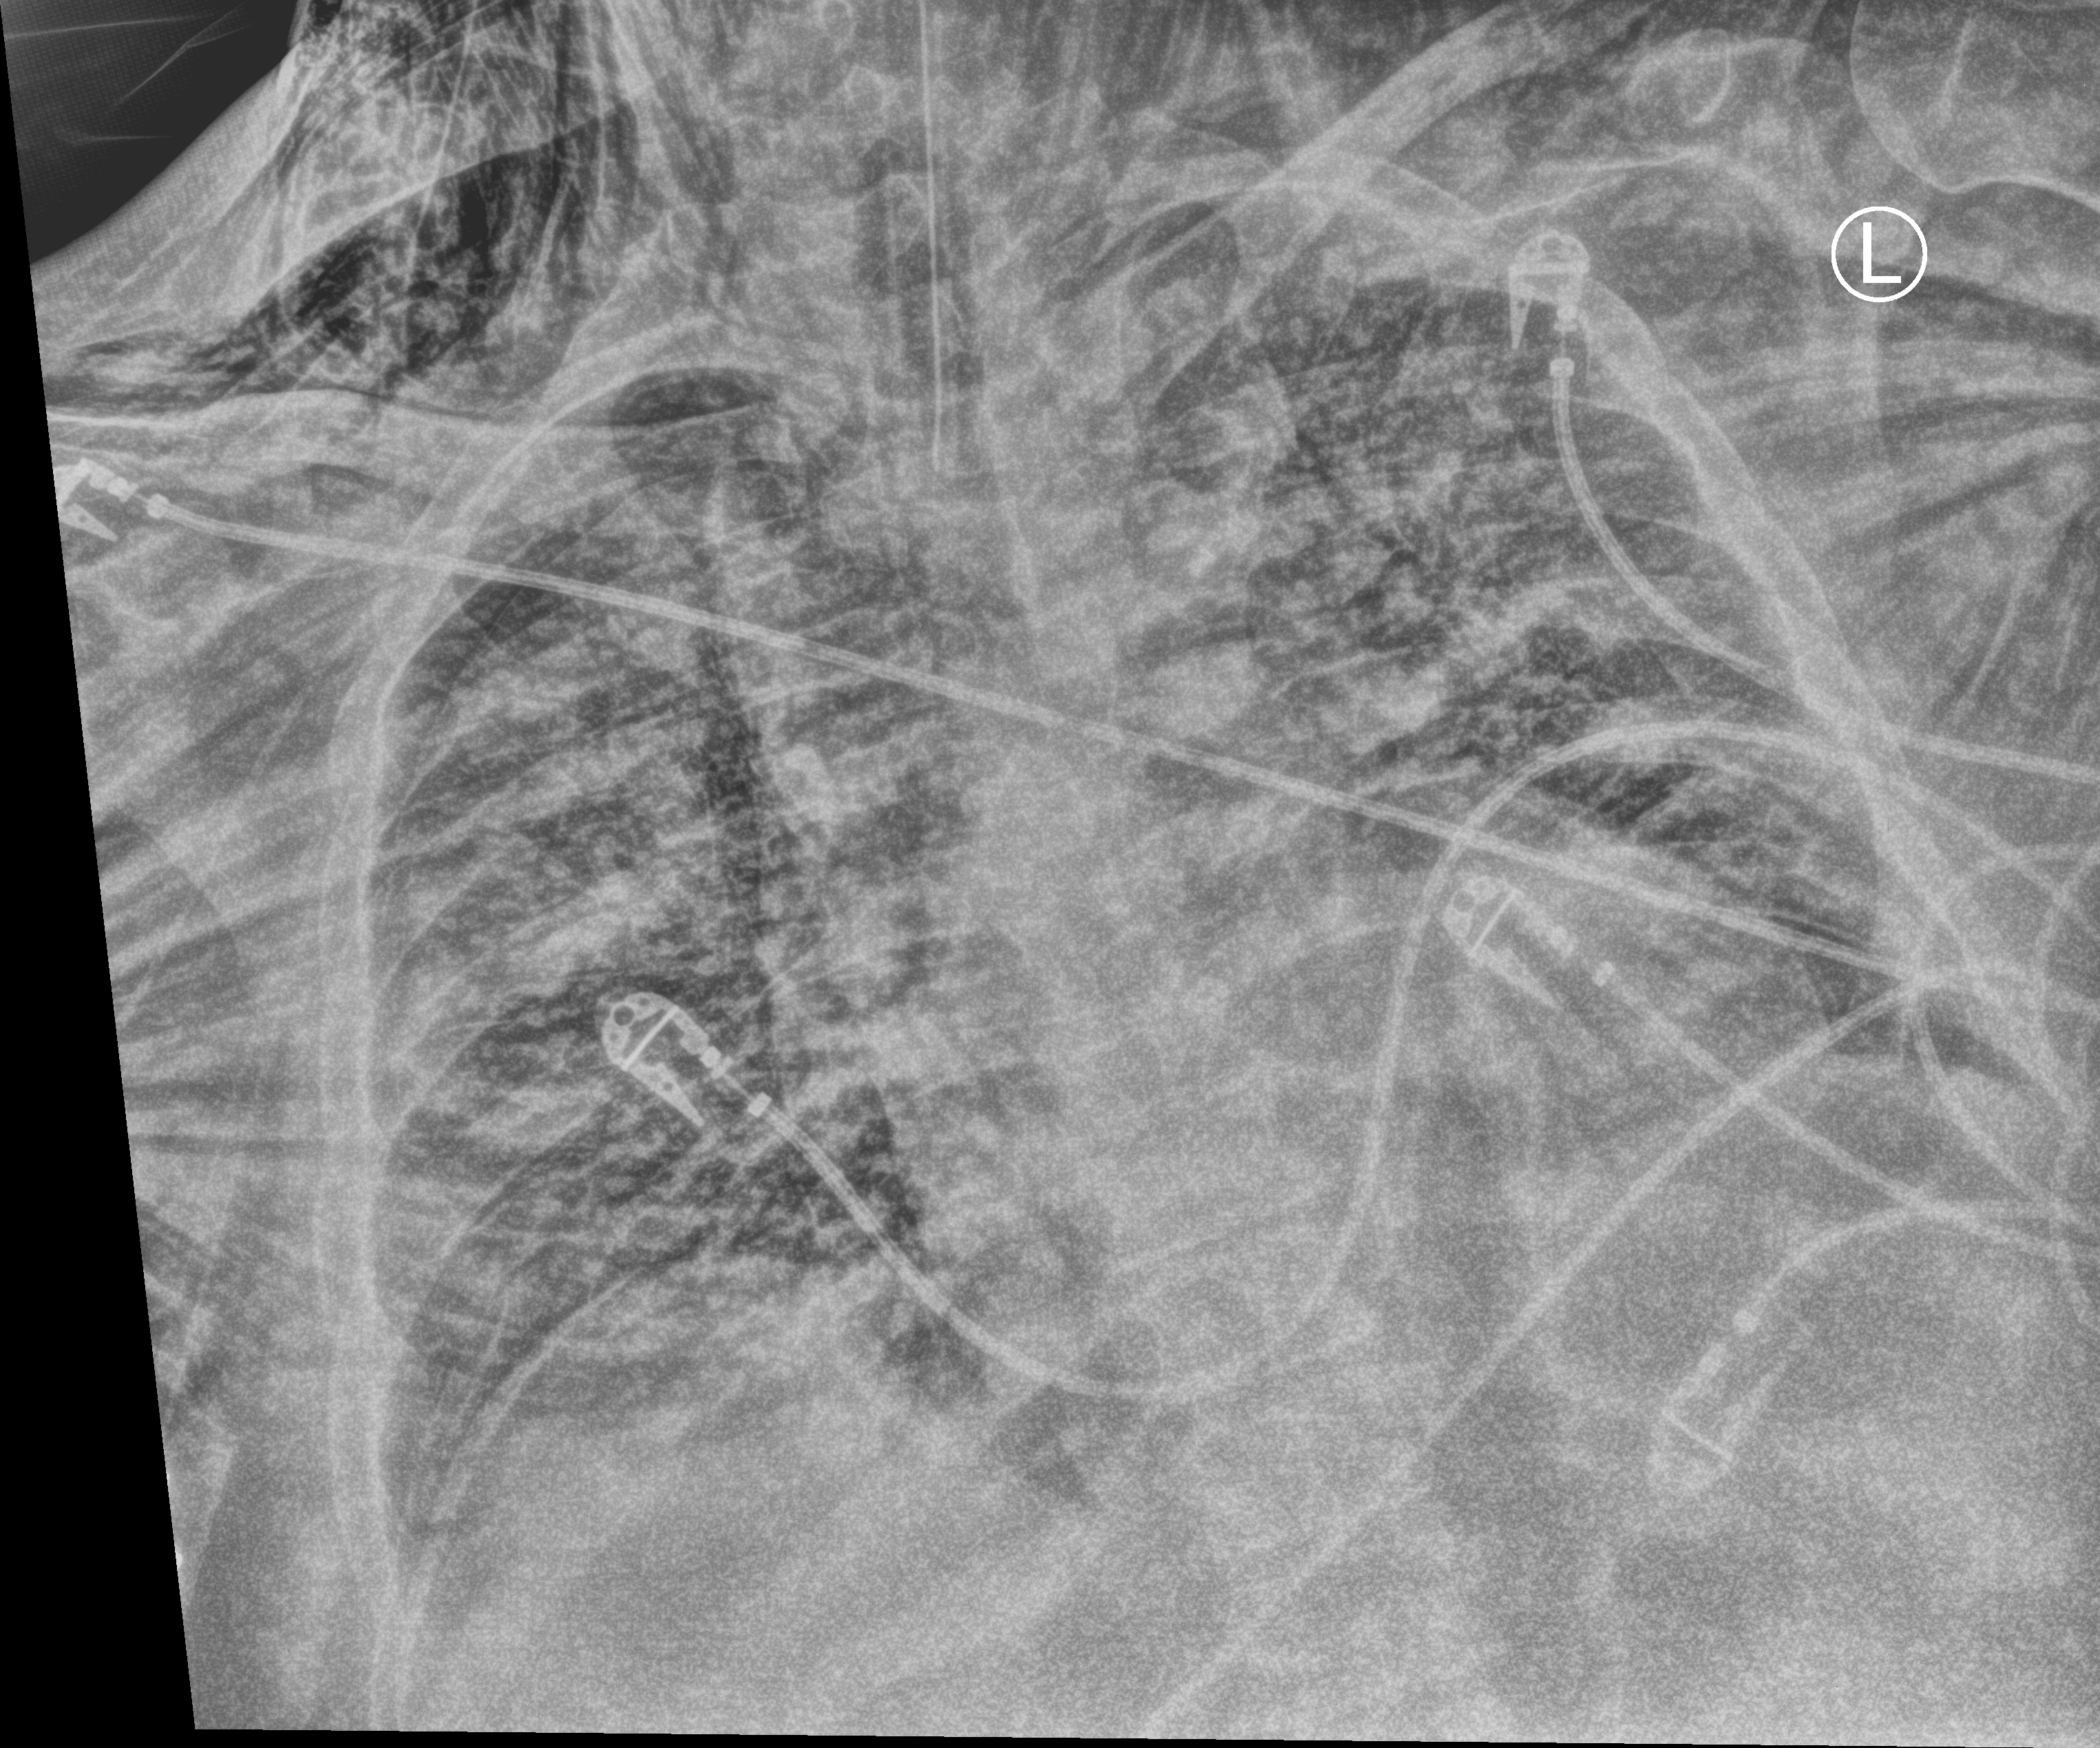
Chest X-ray (portable), anteroposterior (AP) projection. Patient hospitalised with COVID-19, aged 18–59 years.
Hospital-stay facts (about this admission, not read from this image; timing relative to this image not recorded): admitted to intensive care during this hospital stay: yes; mechanically ventilated during this hospital stay: yes; COPD (admission record): no.